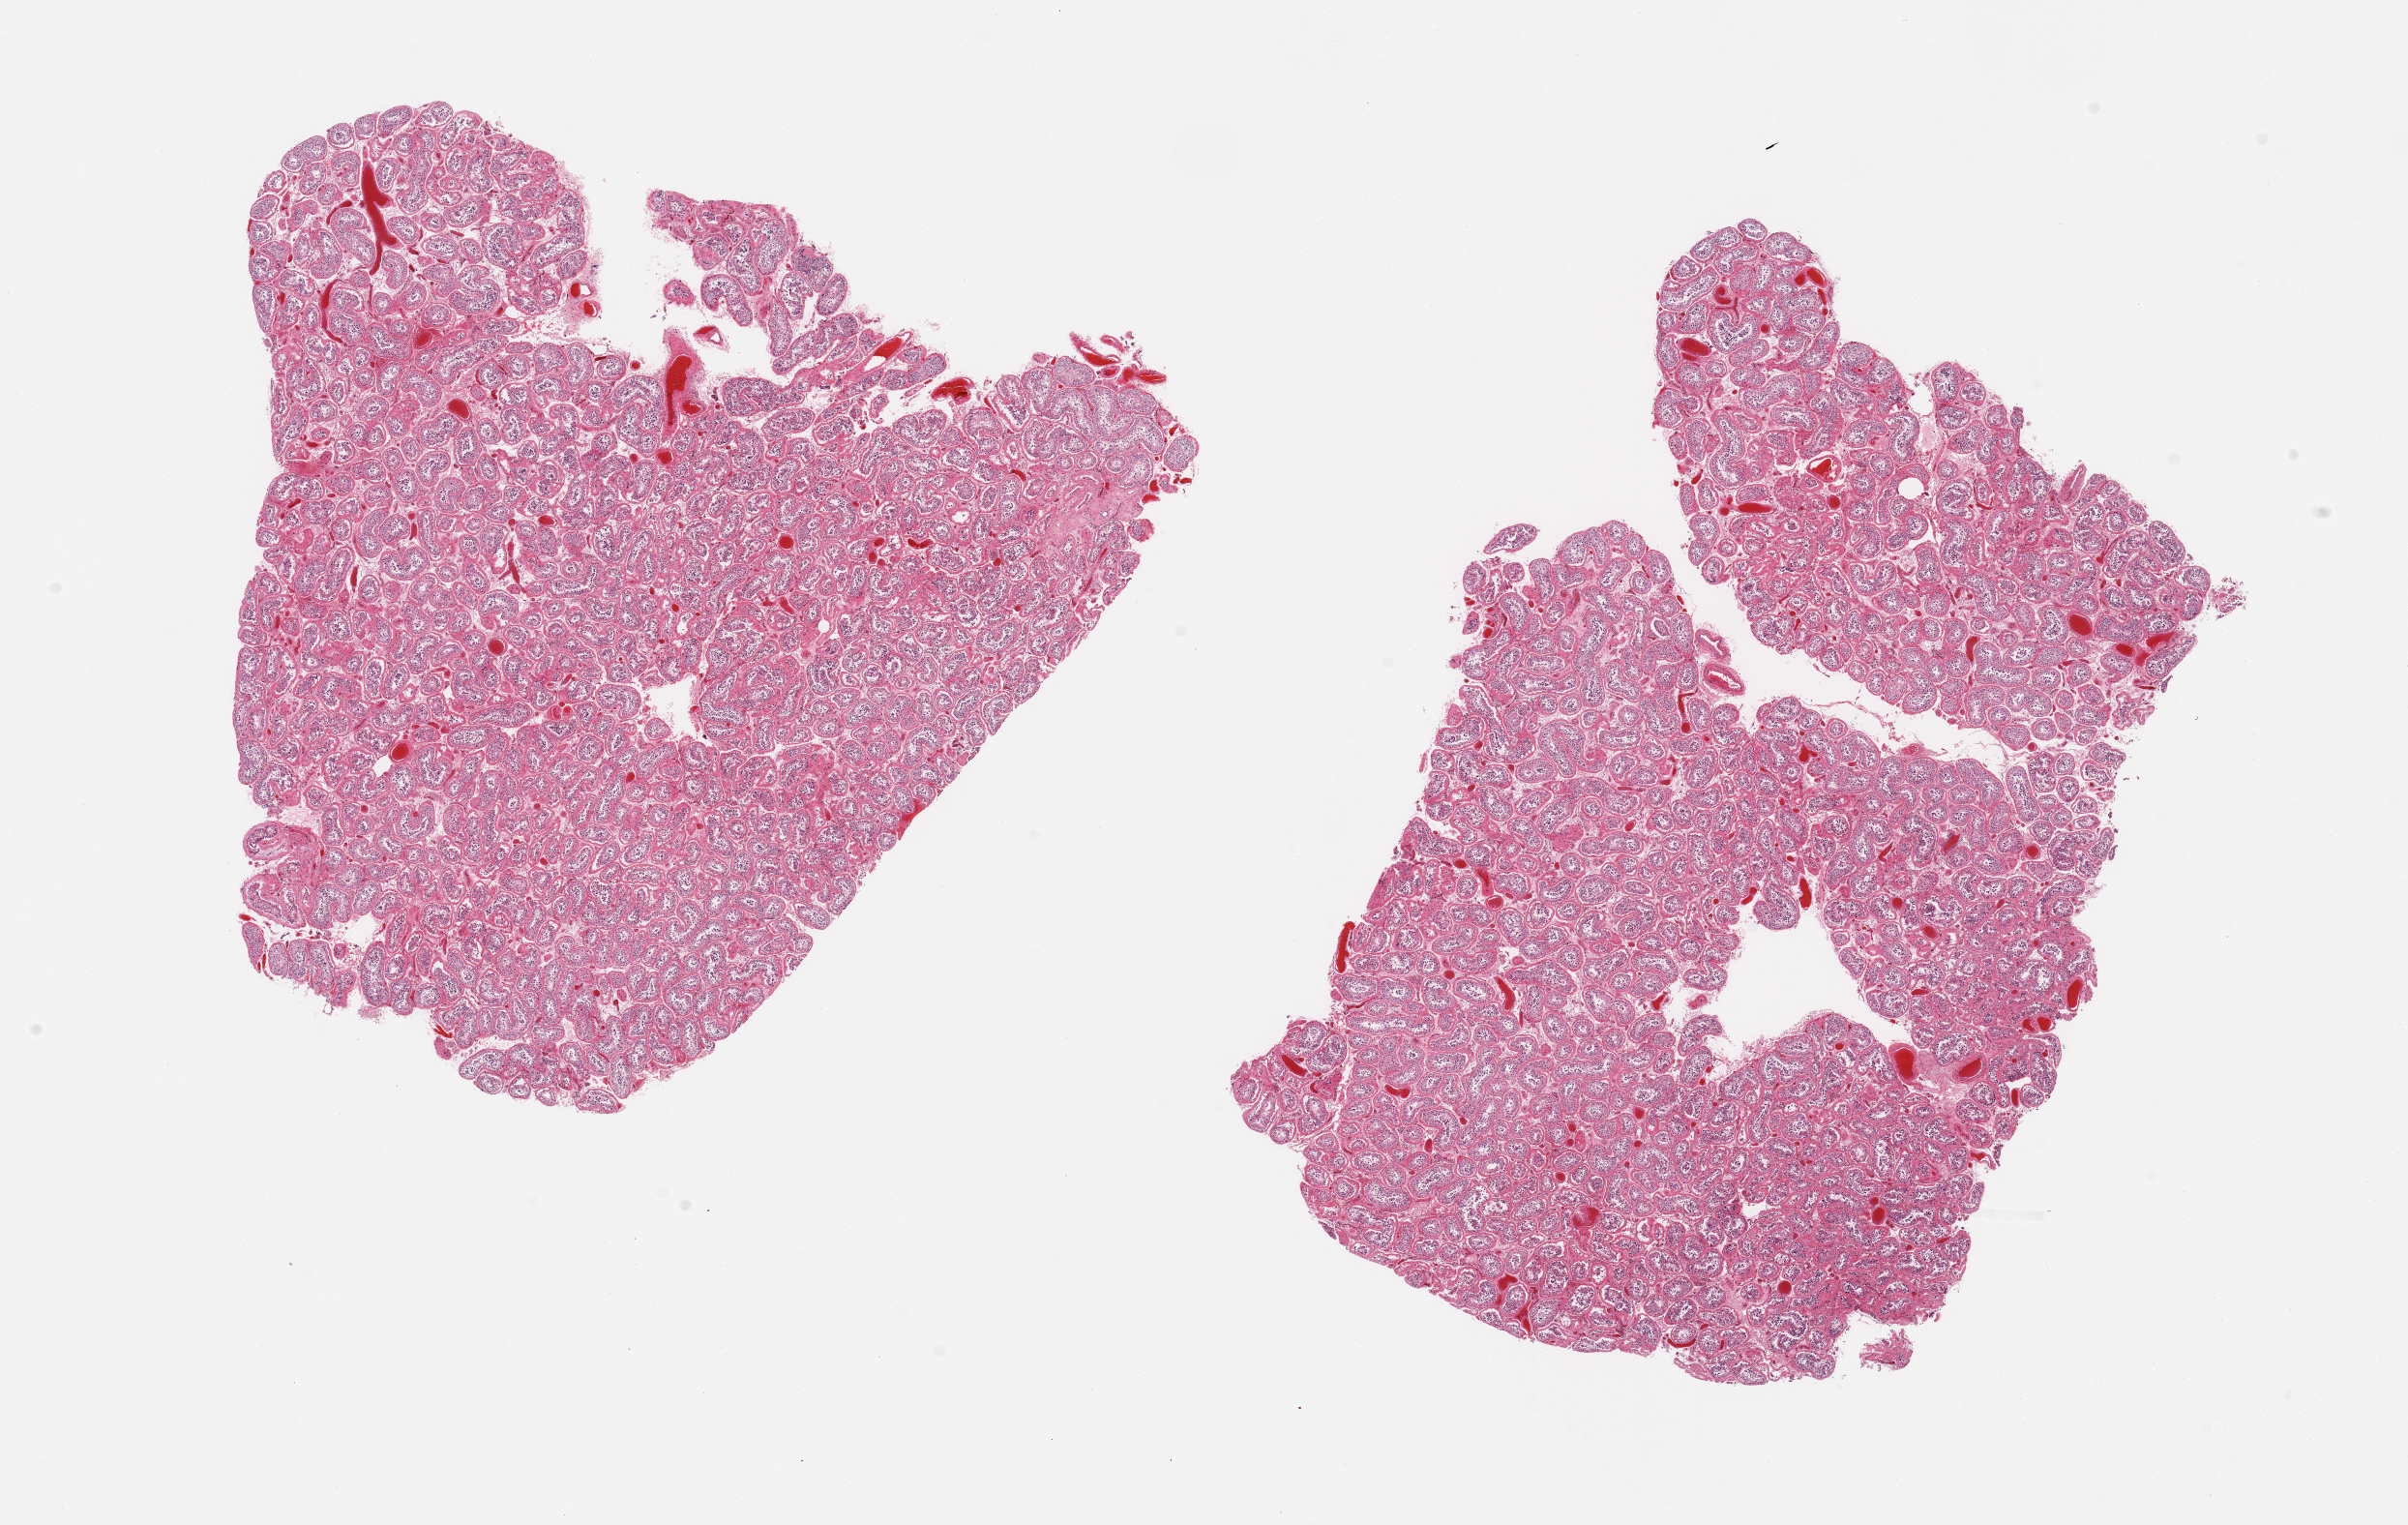
Hematoxylin and eosin (H&E) whole-slide image, shown as a low-resolution overview of the whole scanned area (about 19.7 x 12.5 mm, slide scanned at 20x); PAXgene-fixed paraffin-embedded (PFPE) section; sampled site (target tissue): testis; donor tissue sample. Male donor.
• pathologist's review note for this sample: 2 pieces, spermatogenesis appears reduced